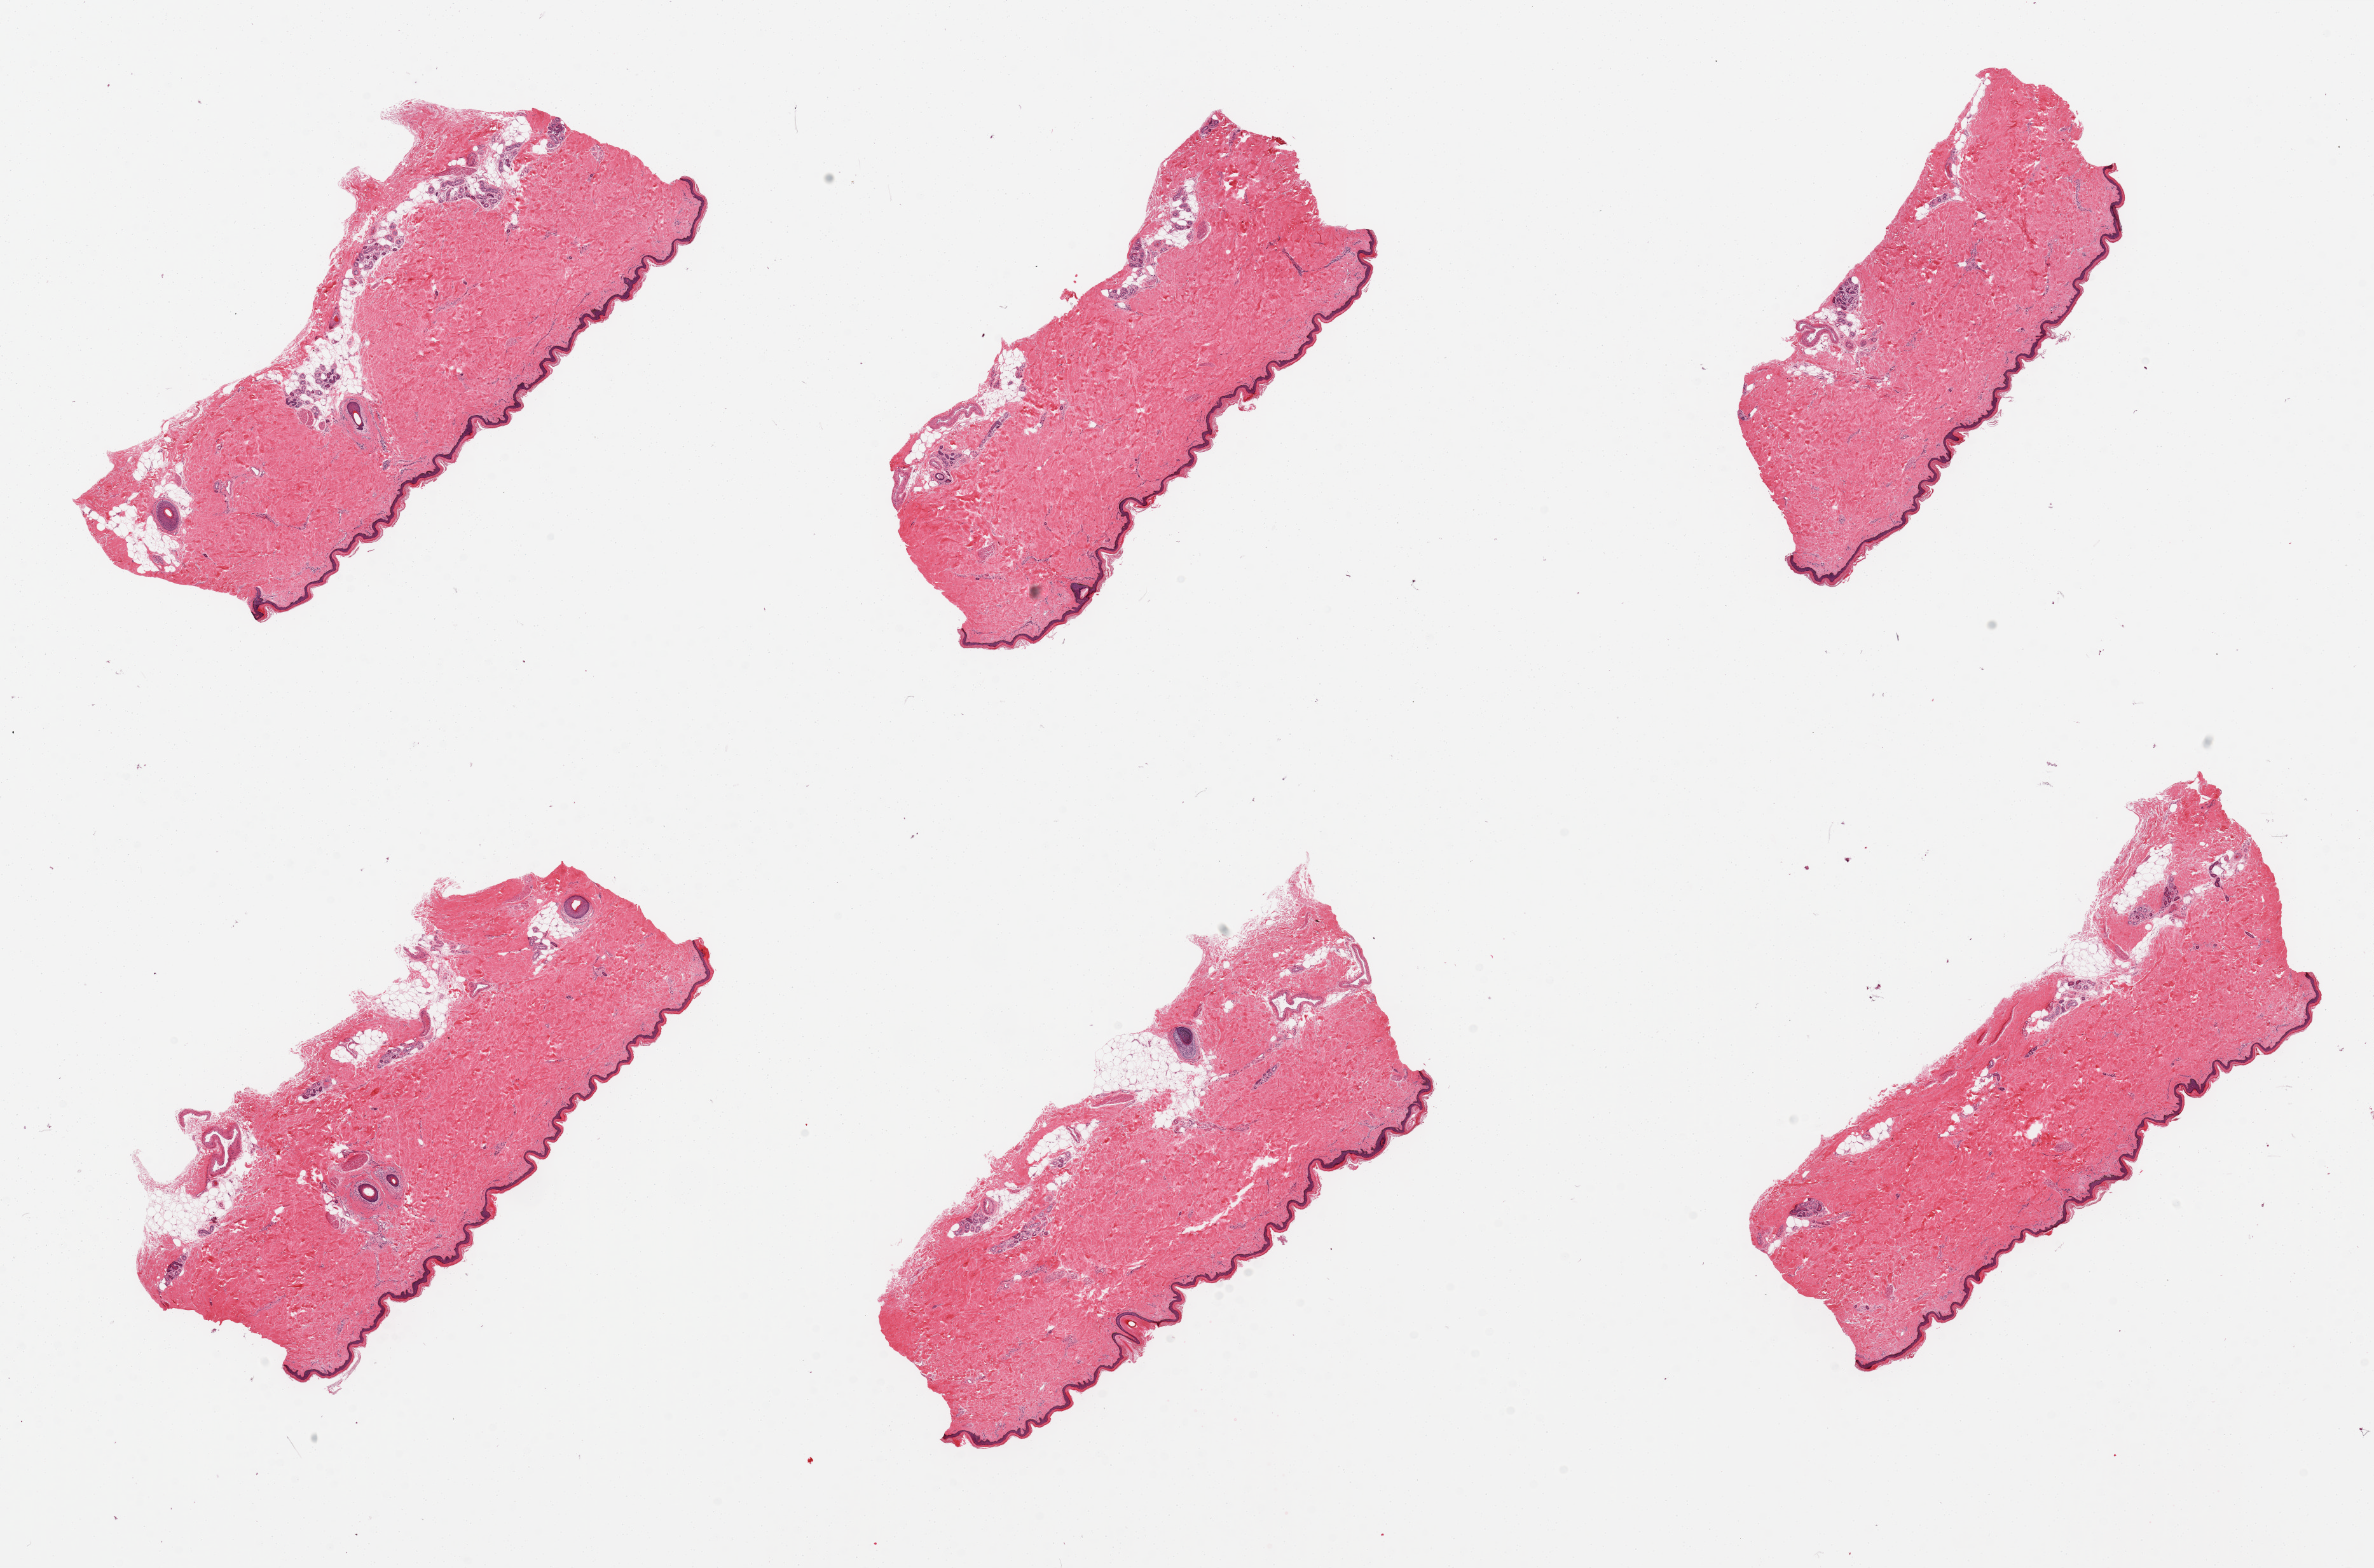
Digitized hematoxylin and eosin (H&E)-stained section, brightfield — whole scanned area (about 29.5 x 19.5 mm, acquisition: 20x scan) shown as a low-resolution overview, PAXgene-fixed paraffin-embedded (PFPE) section, target tissue: skin of lower leg, donor tissue sample. Donor: male.
Review note (as recorded): 6 pieces, predominantly well trimmed, up to 10% internal and attached fat, squamous epithelium measures 30-40 microns thick.